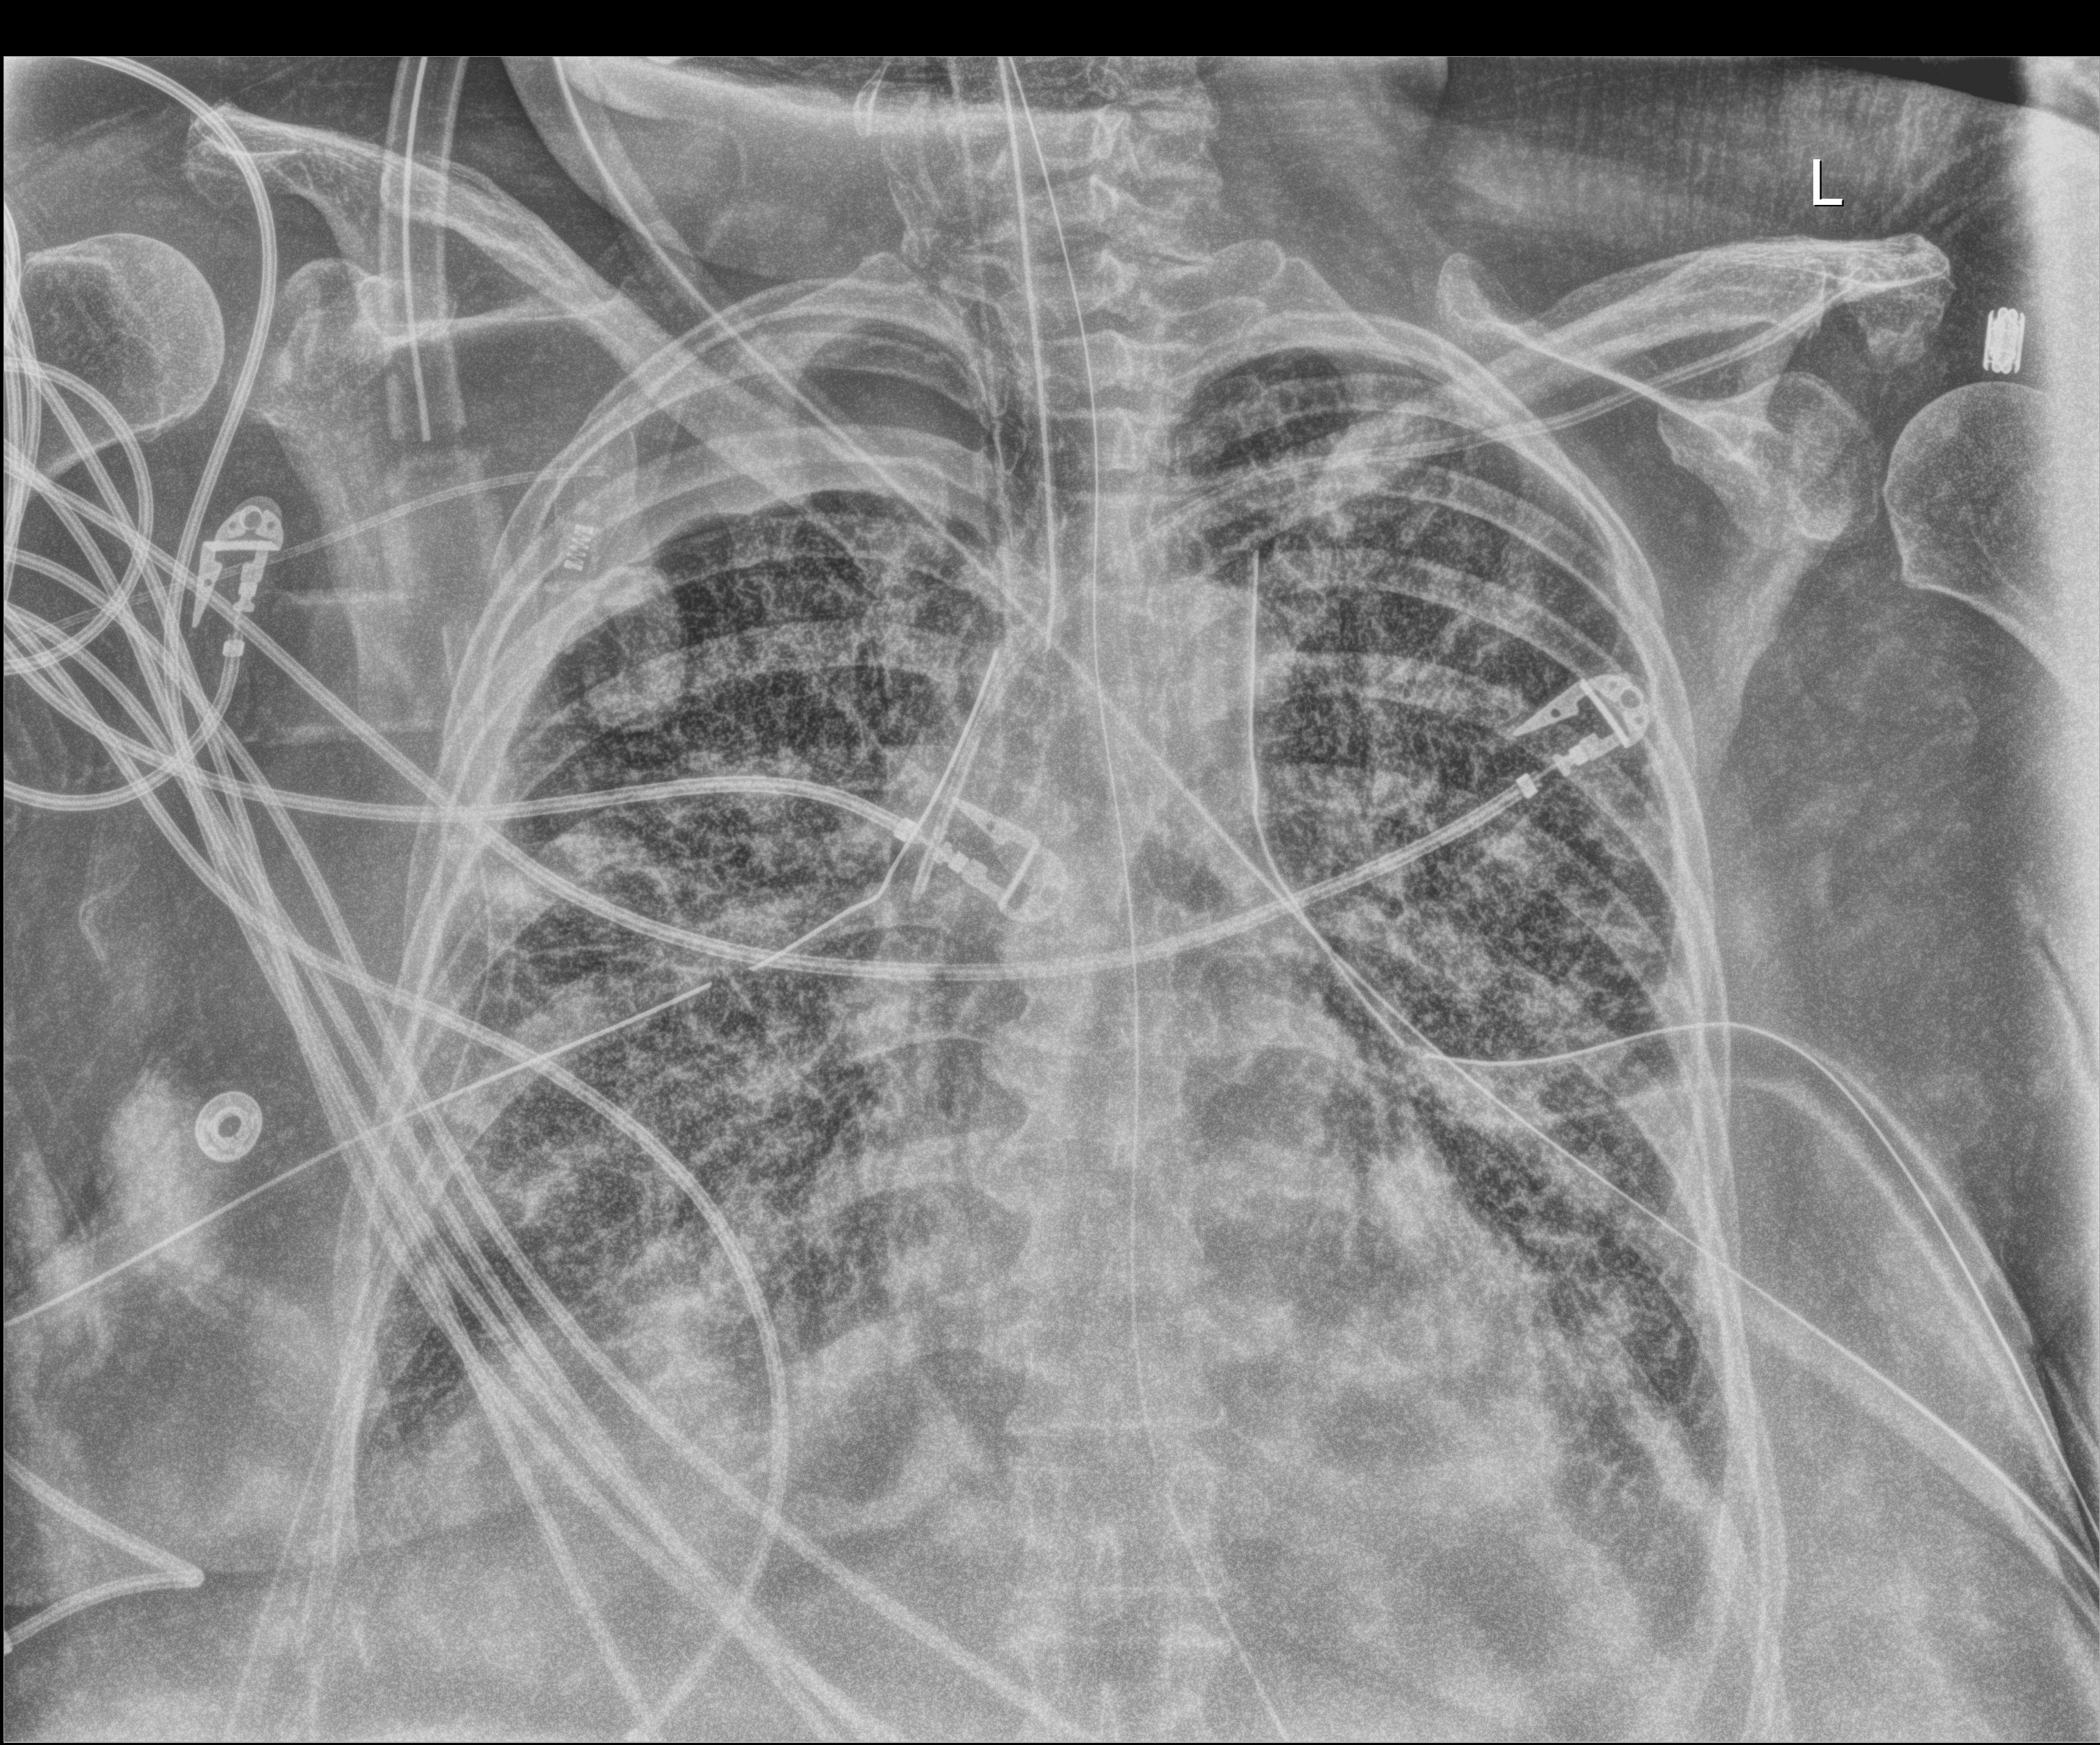
Chest X-ray (portable). Patient hospitalised with COVID-19; female, aged 60–74 years.
Hospital-stay facts (about this admission, not read from this image; timing relative to this image not recorded): mechanically ventilated during this hospital stay: yes; admitted to intensive care during this hospital stay: yes.